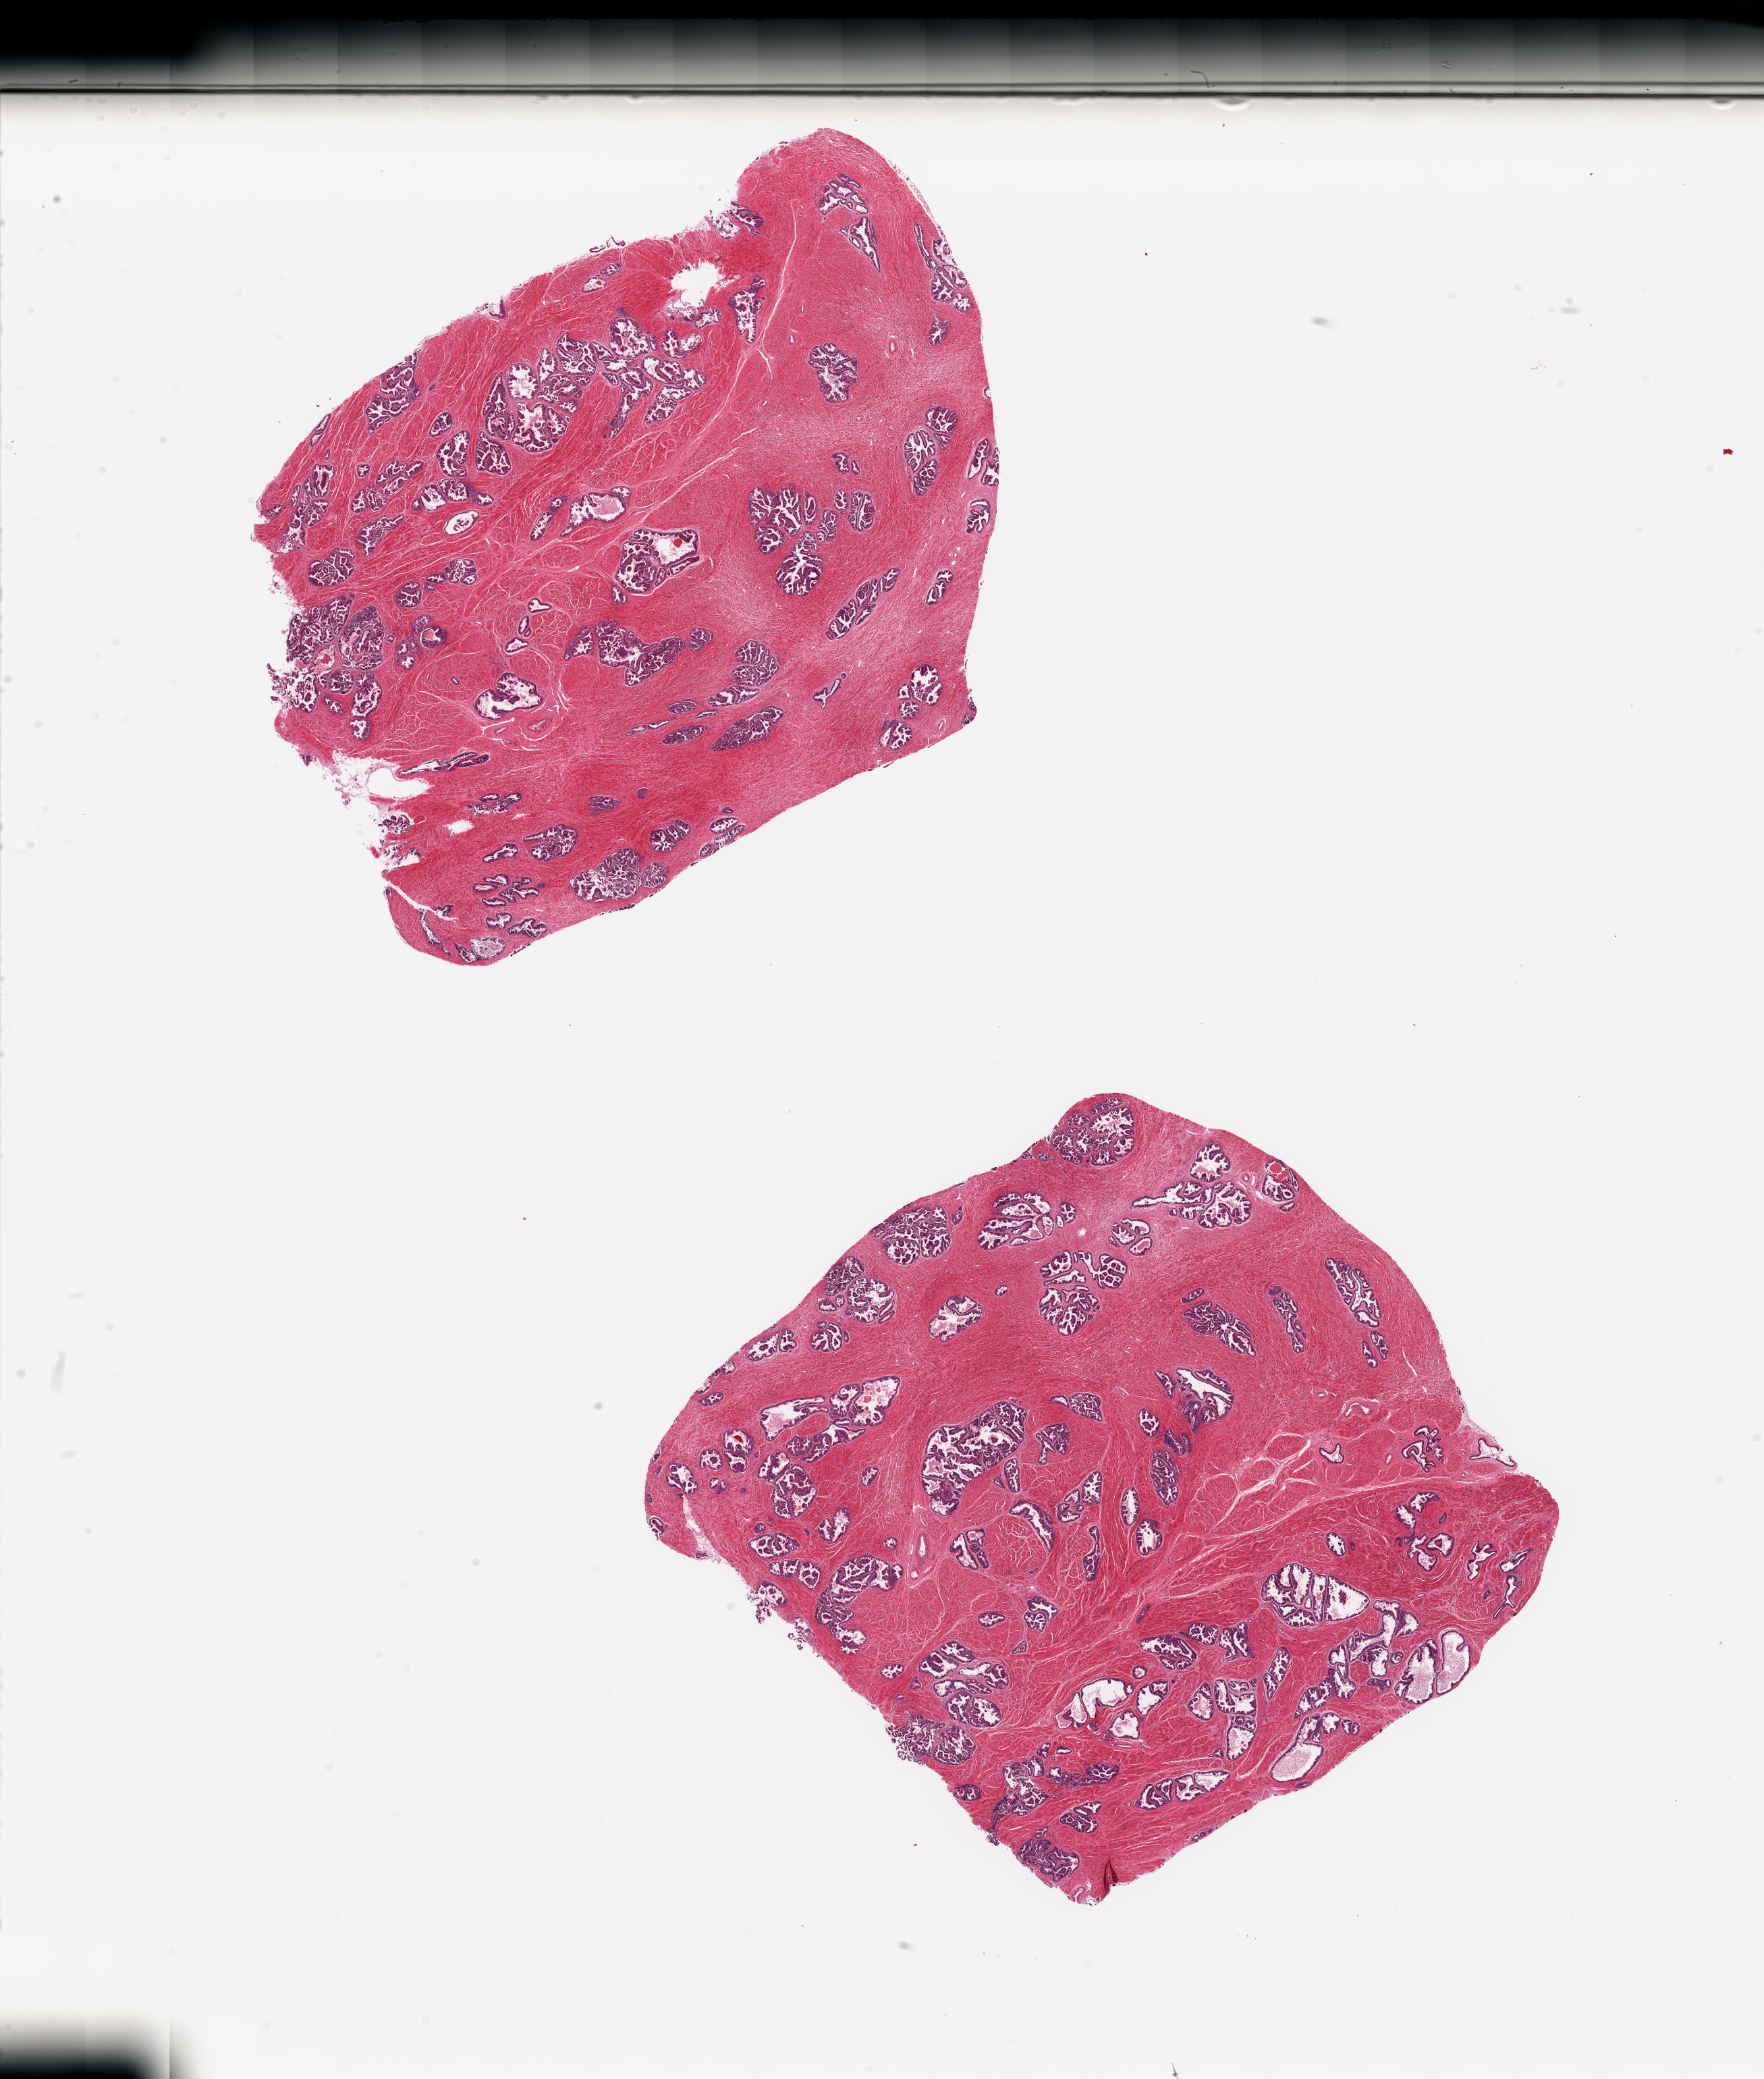
Haematoxylin and eosin whole-slide image, brightfield — whole scanned area (about 20.7 x 24.4 mm) shown as a low-resolution overview, PAXgene-fixed paraffin-embedded (PFPE) section, section of prostate (target tissue), donor tissue sample. Male donor.
Review note (as recorded): 2 pieces; well preserved glands.